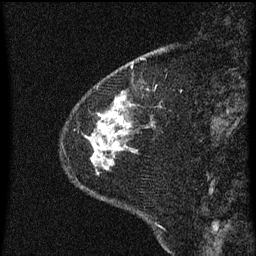
Breast MRI (dynamic contrast-enhanced), one sagittal slice. Slice 13 of 60 in the series (ordered by position). Dynamic contrast-enhanced series, image 2 of 3 at this slice position (ordered by acquisition). 1.5 T. TE 4.2 ms, TR 8 ms. 2 mm slice thickness. 256 × 256 image matrix, field of view 180 × 180 mm. Patient: female, 60 years.
Structures marked on this image (semi-automatic segmentation, software-assisted and operator-edited):
- analysis volume of interest (the breast-tissue region the enhancement analysis was run in; not a lesion): bounding box (x1, y1, x2, y2) in pixels: (87, 86, 159, 175)
- tumour enhancement mask (voxels above the 70 % enhancement threshold inside the analysis volume of interest): (93, 100, 124, 161)